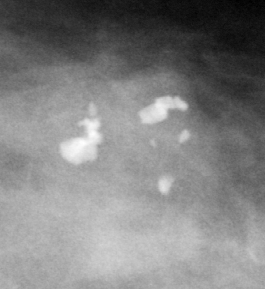
Crop from a digitized film mammogram around one marked abnormality, left breast, CC view.
Calcifications, morphology dystrophic, distribution clustered; BI-RADS assessment category 2; subtlety rating 5 on a 1 (subtle) to 5 (obvious) scale; benign; no additional work-up was recommended (benign without callback).